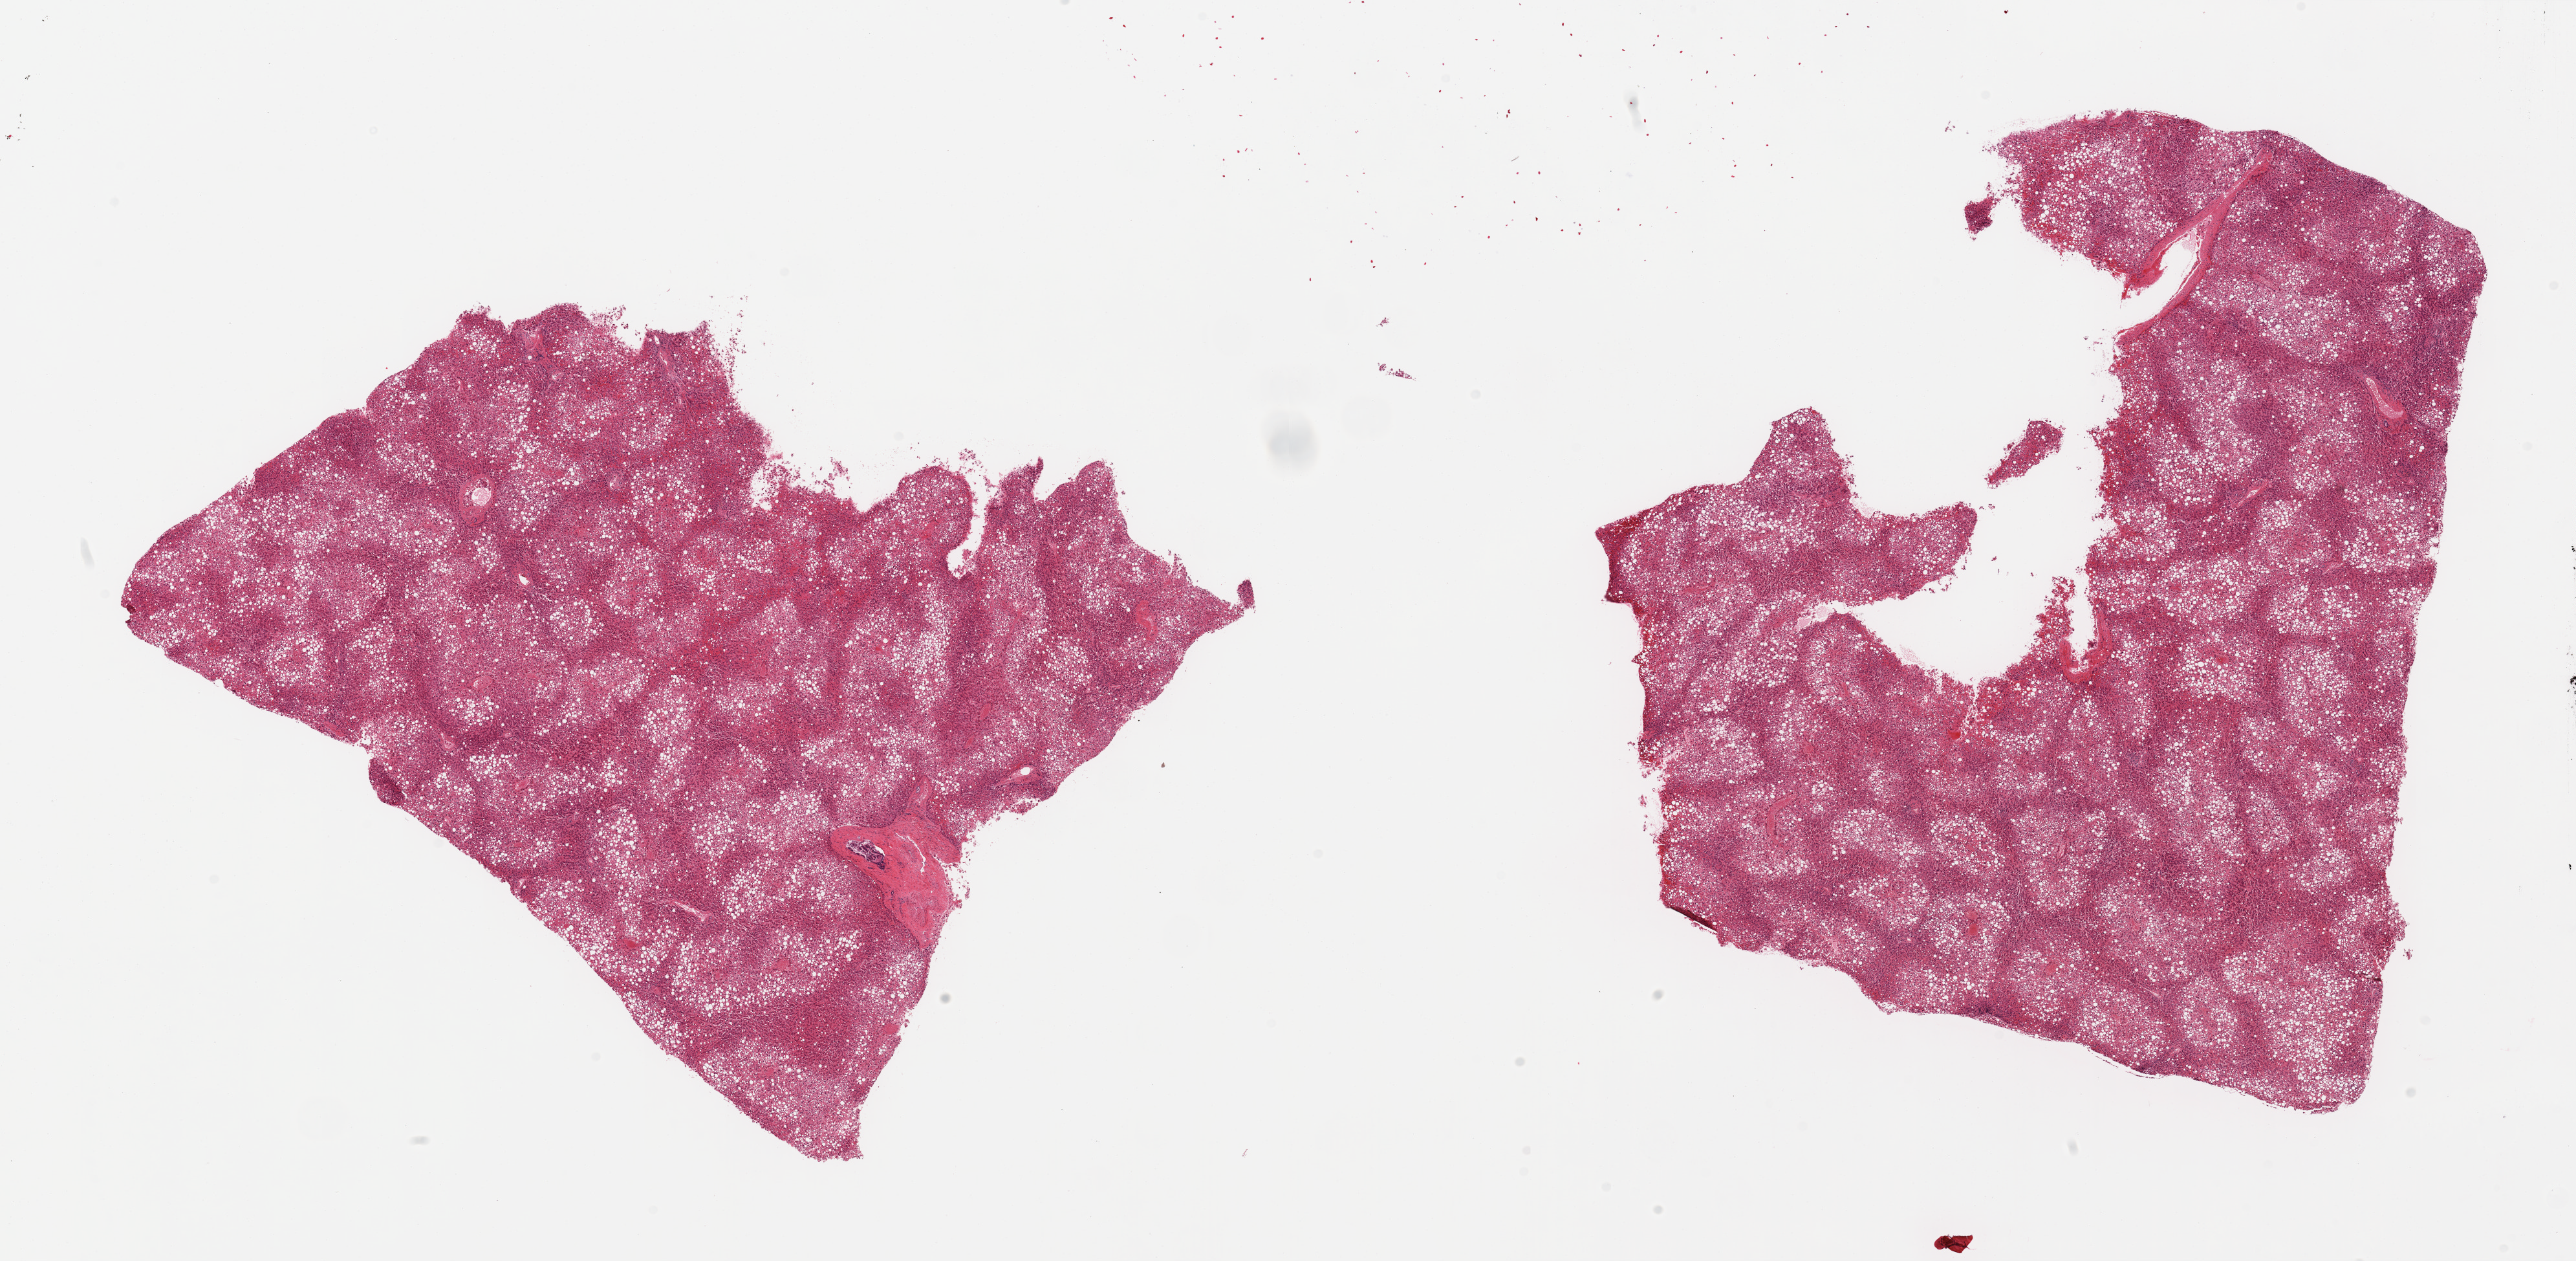
Hematoxylin and eosin (H&E) whole-slide image — low-resolution overview of the scanned area, about 31.5 x 15.4 mm, PAXgene-fixed, paraffin-embedded tissue, section of liver (target tissue), donor tissue sample. Donor sex: male.
Reviewer comment on this tissue sample: 2 pieces; severe steatosis, congestion.